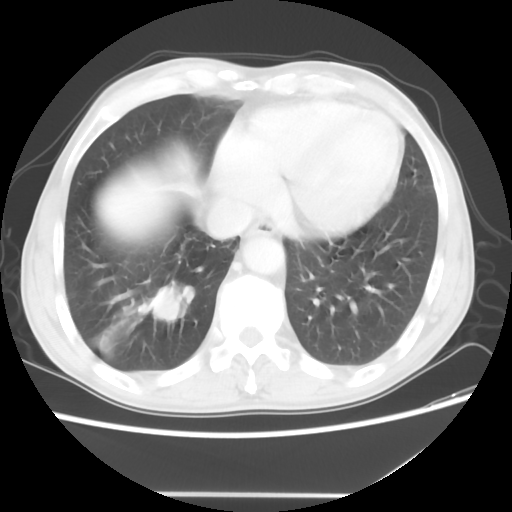
Chest CT, one axial slice. Slice 14 of 56 in the series (ordered by position). Reconstruction kernel STANDARD. Lung window (W 1500 / L -600 HU). 512 × 512 image matrix, field of view 344 × 344 mm. Male patient, age 65 years. From the clinical record (not read from this slice): clinical TNM (as recorded): T1c N3 M0.
Annotated regions visible in this slice (bounding box drawn by a radiologist):
- lung tumour (recorded histology: small cell carcinoma): box from (x=137, y=278) to (x=195, y=327) px